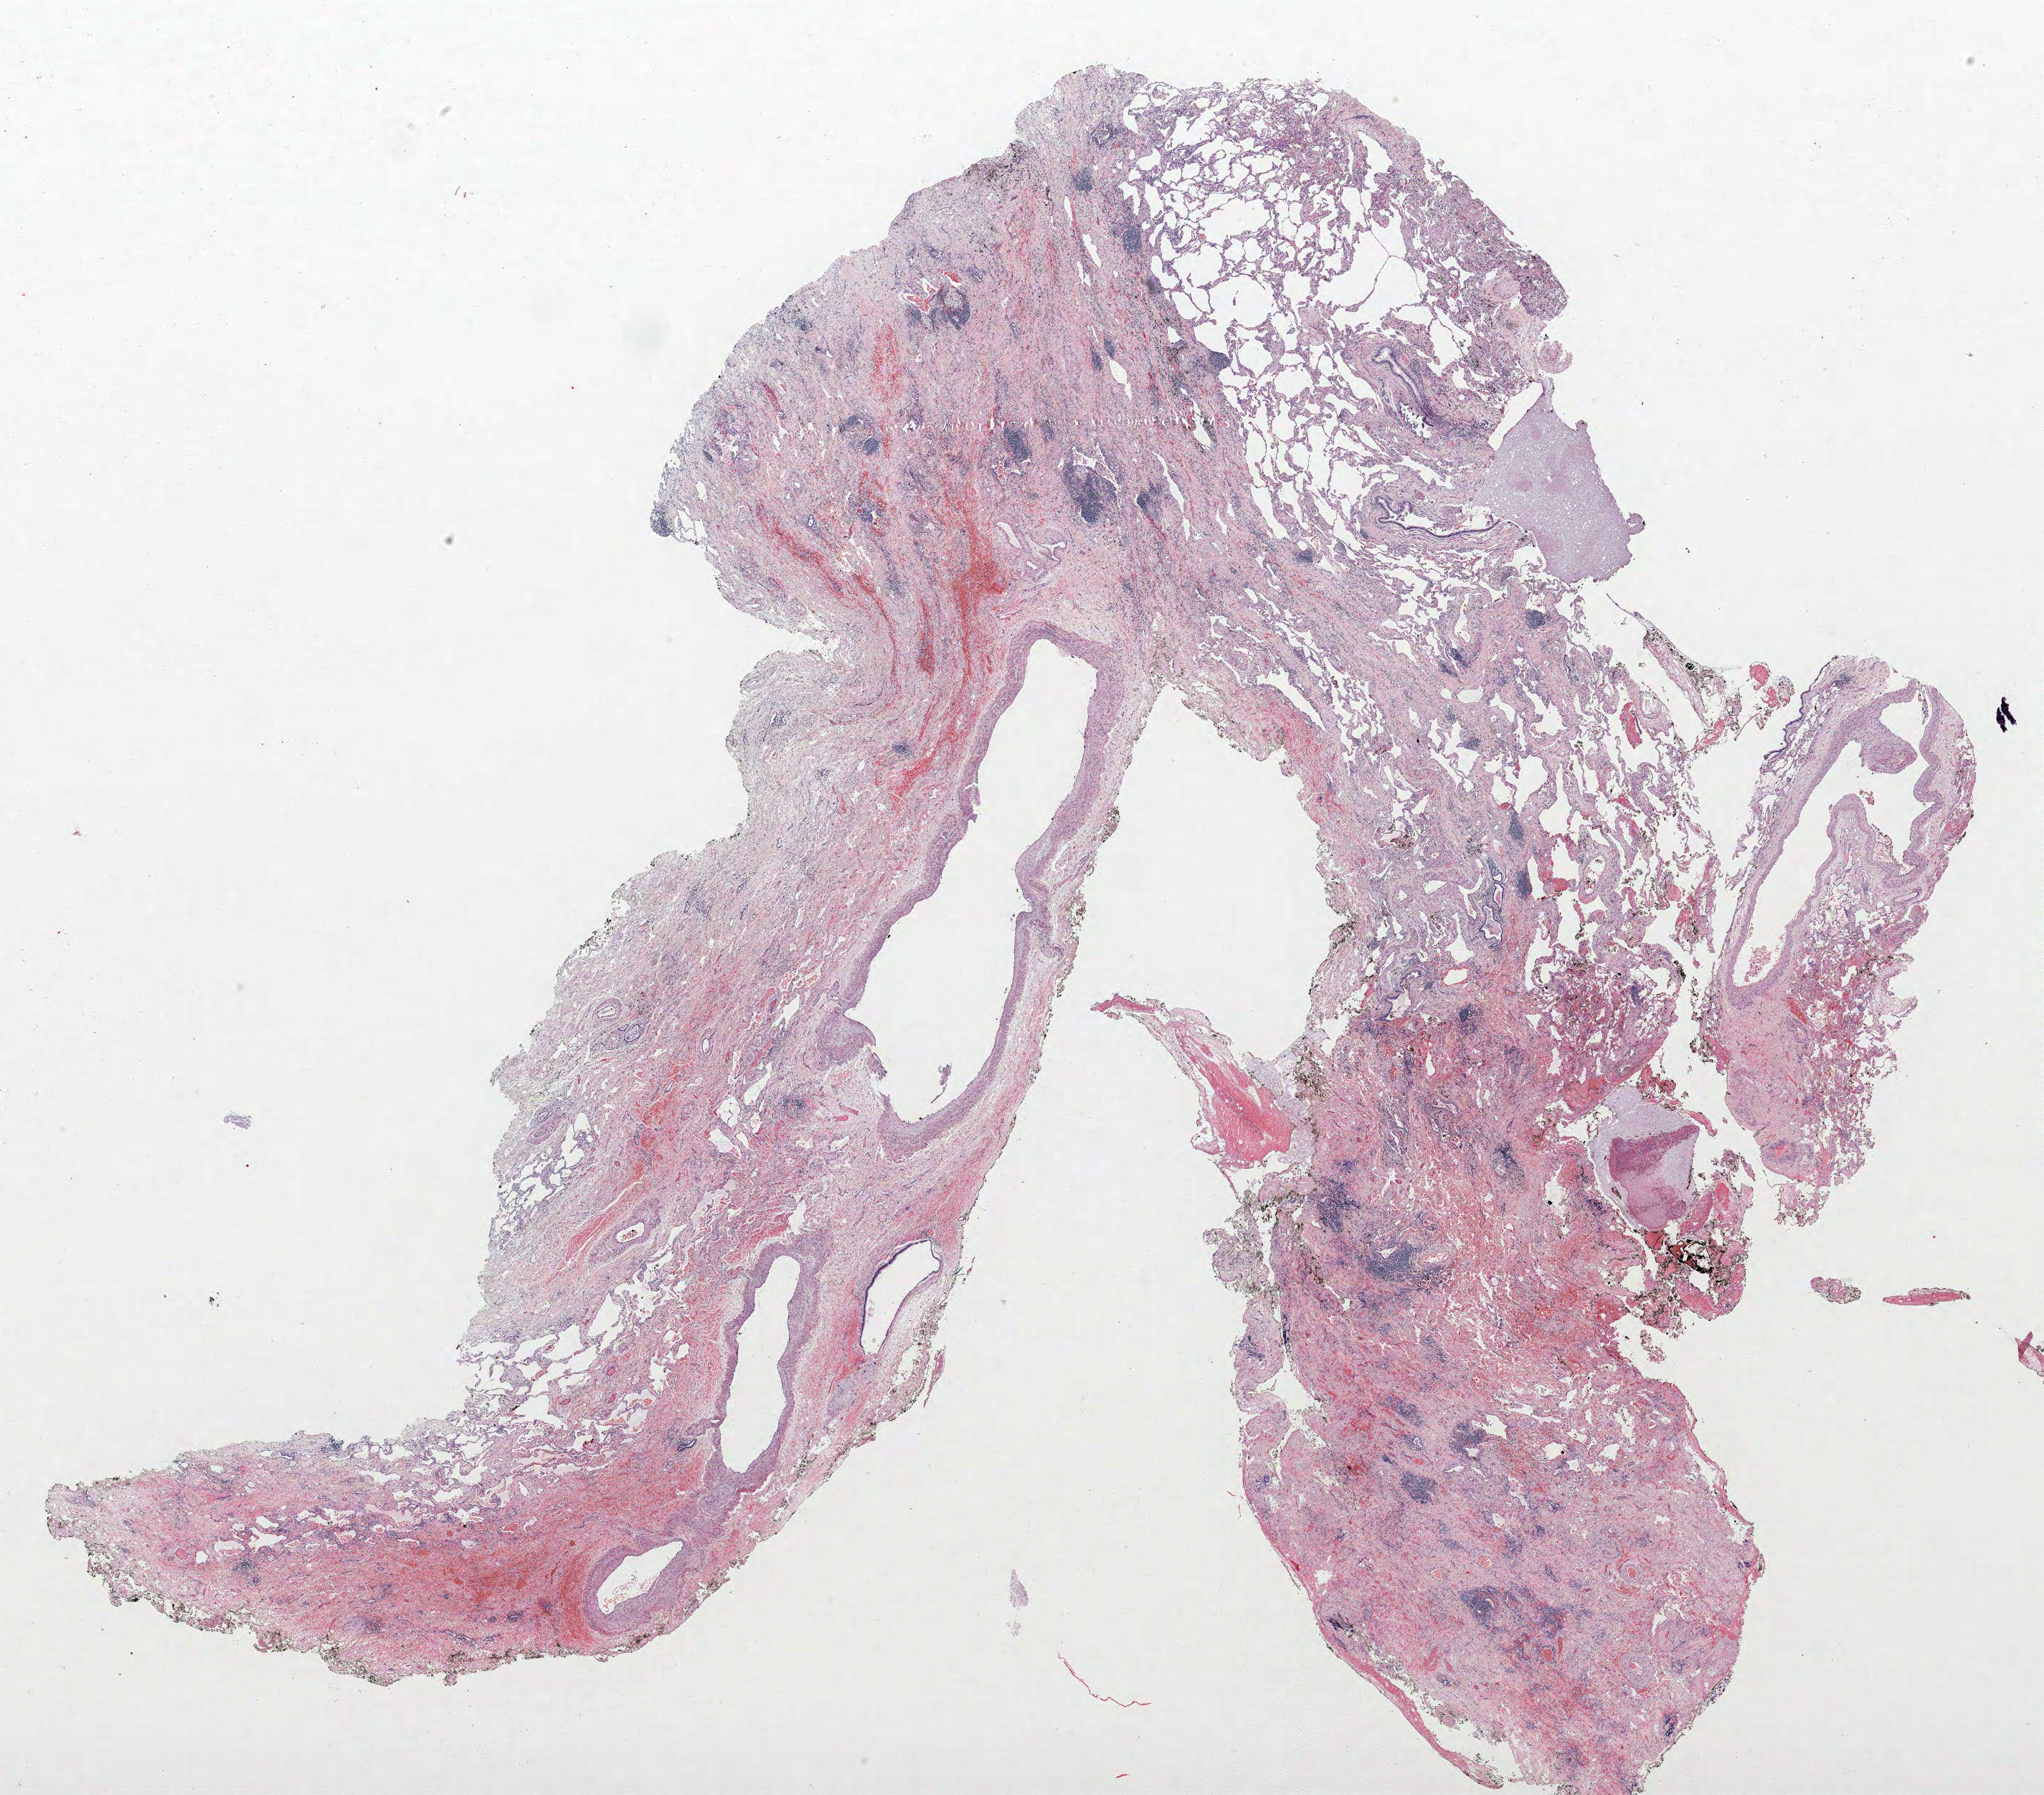
H&E-stained whole-slide image, low-resolution overview of the scanned area, about 22.8 x 20.0 mm; formalin-fixed paraffin-embedded (FFPE) section; lung tissue. Female patient, aged 63 at enrolment. Former smoker at enrolment. Grade: moderately differentiated (G2).
Participant's lung-cancer diagnosis: Squamous cell carcinoma, keratinizing, NOS (ICD-O-3 8071/3). Tumour size (pathology): 42 mm. Primary tumour location (clinical record): right upper lobe. Stage (AJCC 6th edition): IIA.